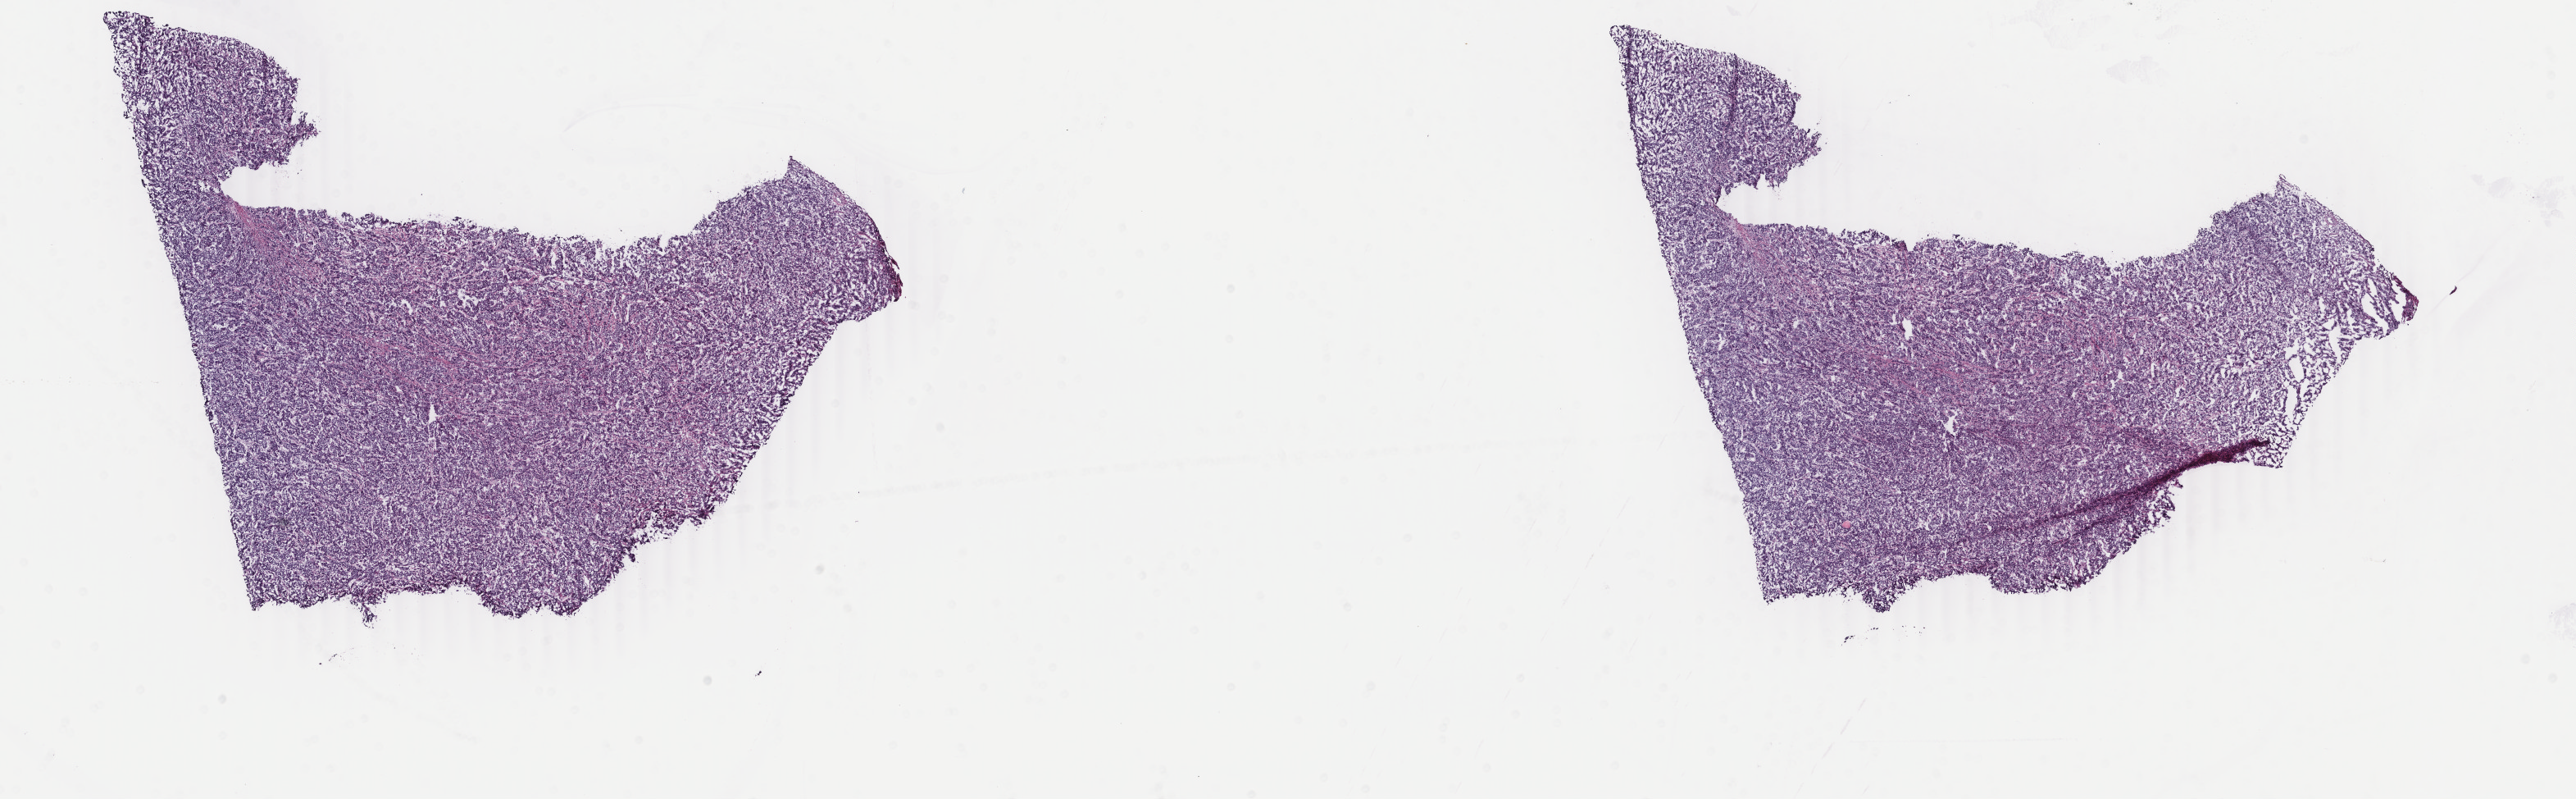
Digitized H&E-stained tissue section (whole slide) — whole scanned area (about 25.0 x 7.7 mm) shown as a low-resolution overview, frozen section from the top of the tissue portion, sample: primary tumour, bladder. Patient: male, age at initial diagnosis 53 years. Pathologist review of this section (percent, as recorded): tumour cells 90%, tumour nuclei 90%.
Pathologic diagnosis: Transitional cell carcinoma.